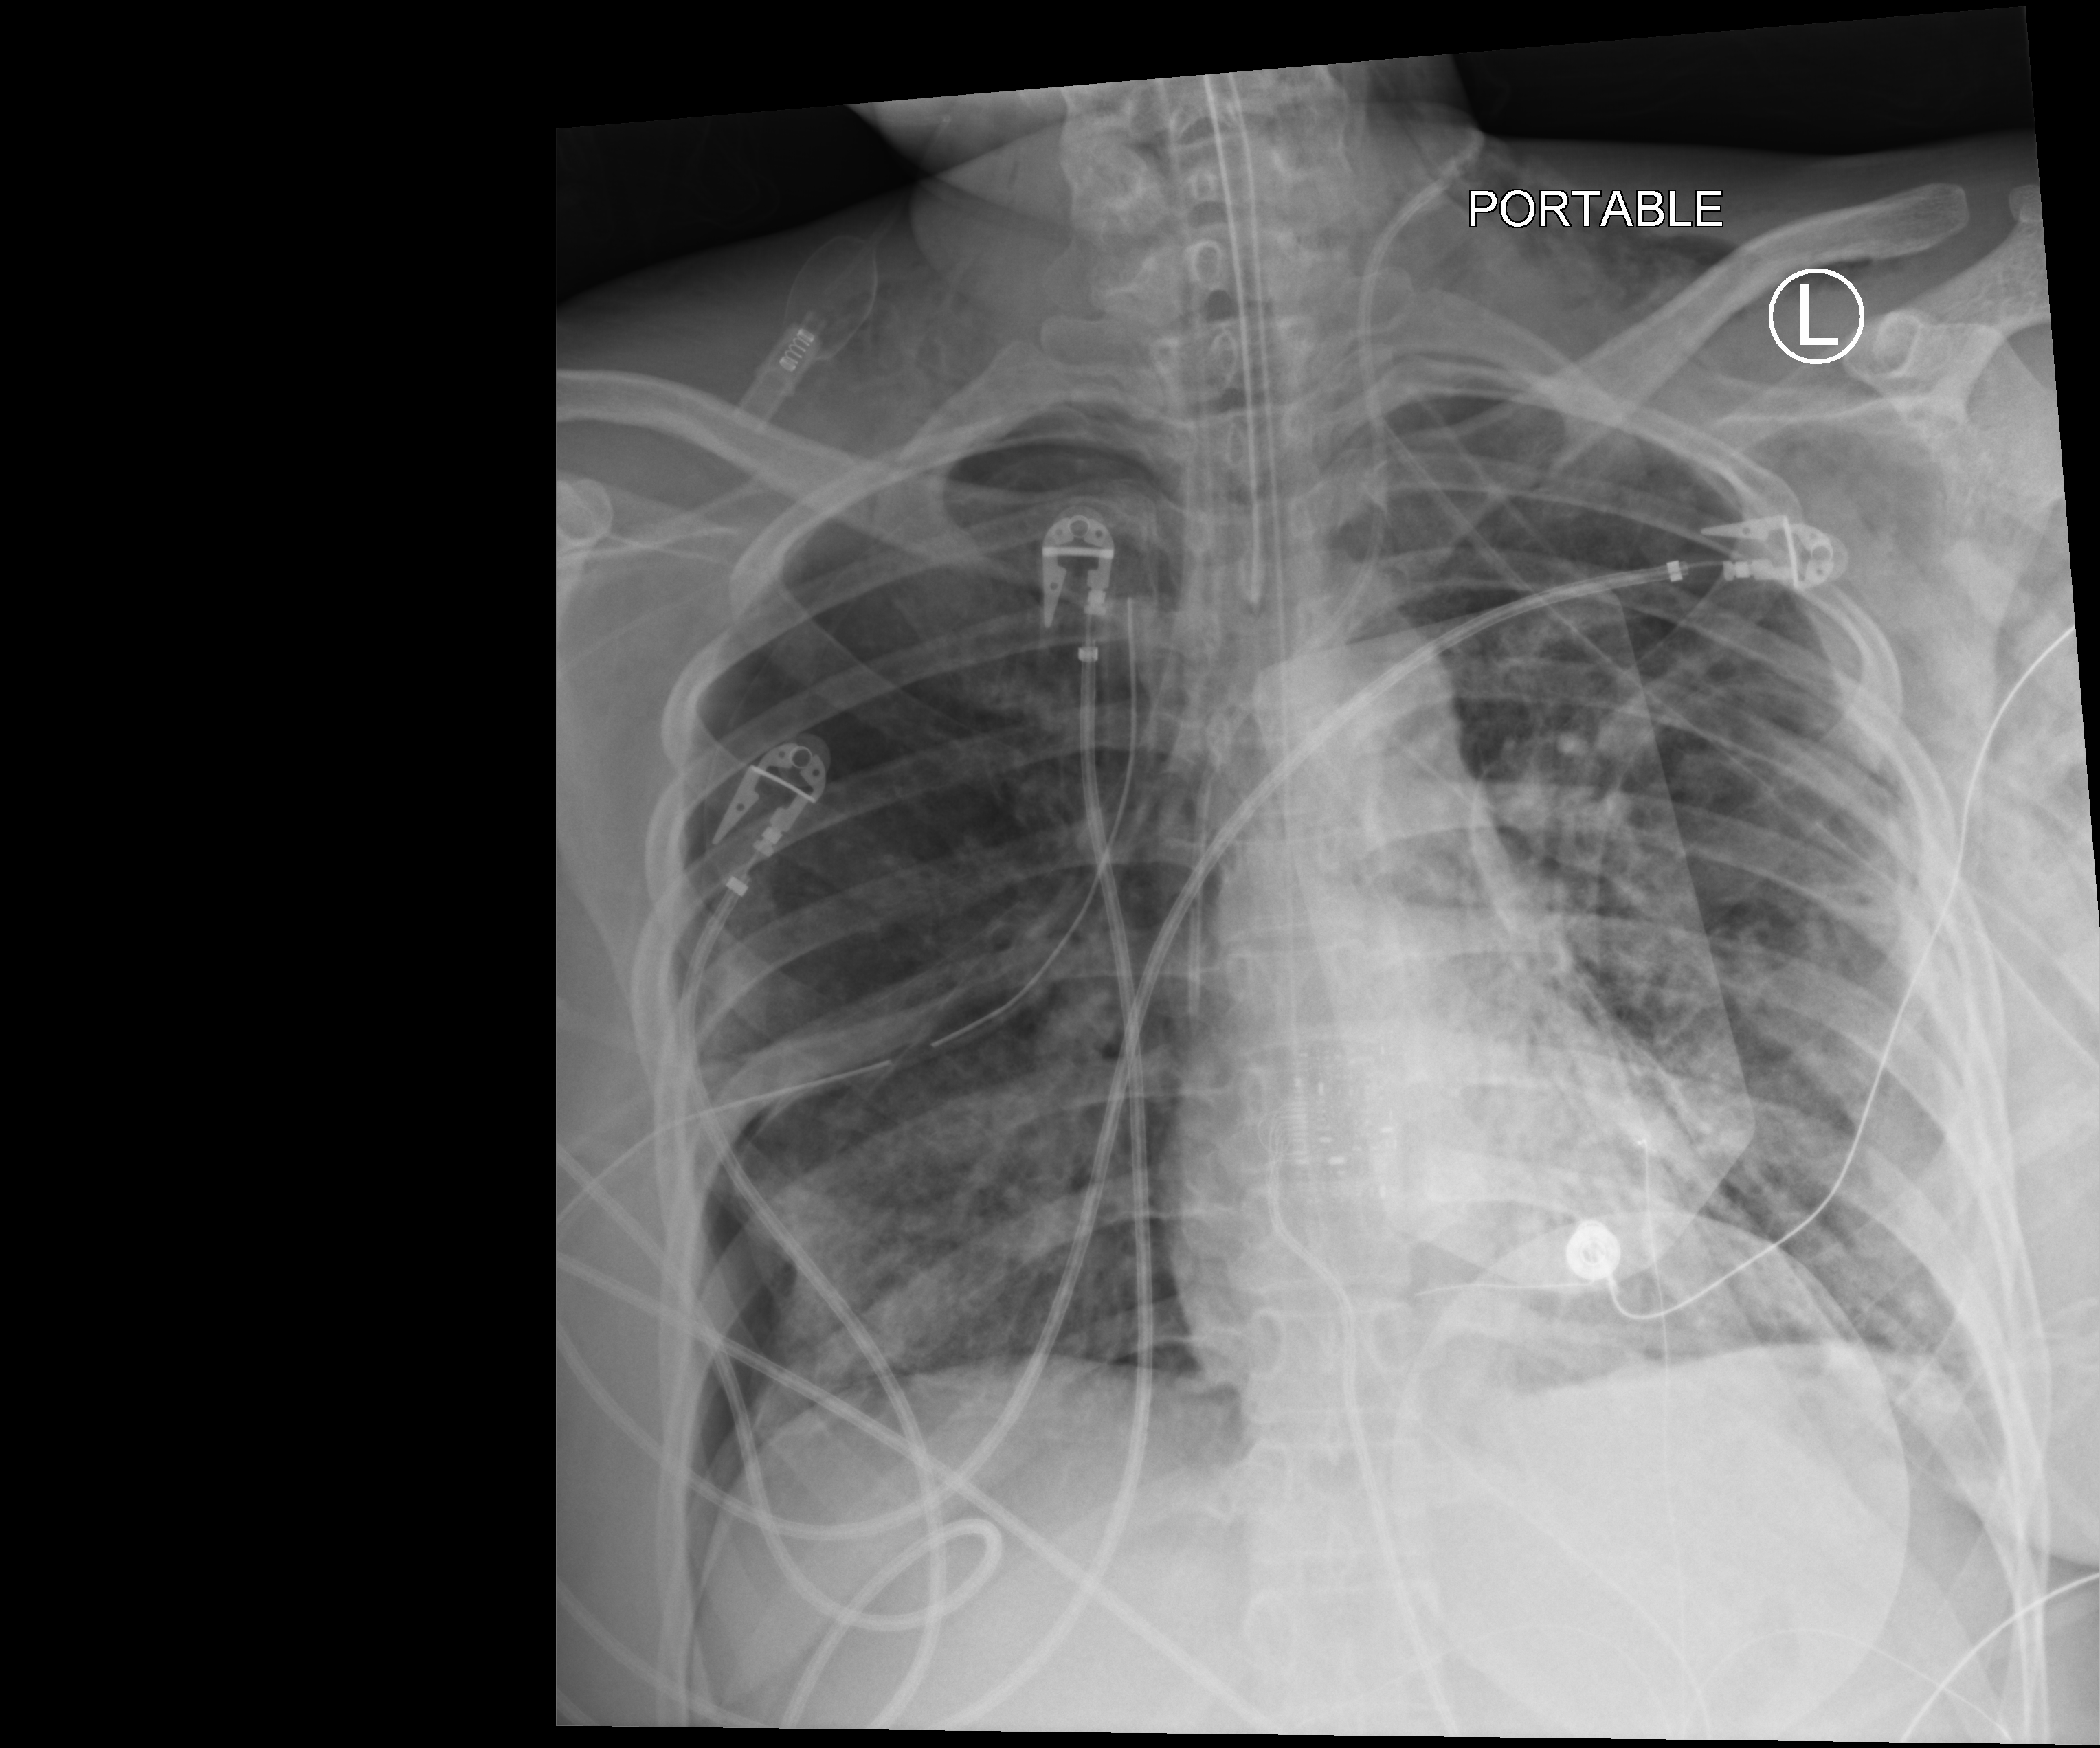
Chest X-ray (portable), anteroposterior (AP) projection. Patient hospitalised with COVID-19, aged 18–59 years.
Admission-level facts for this patient (not findings on this image; timing relative to this image not recorded): other chronic lung disease (admission record): no; diabetes (admission record): no.